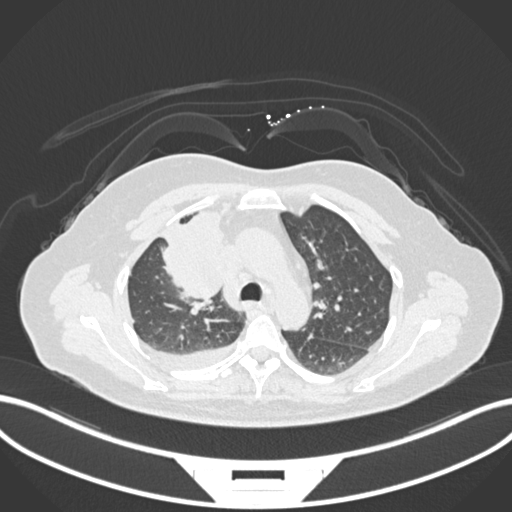
Chest CT, one axial slice. Position 109 of 172 along the scan axis. Reconstruction kernel B30f. 120 kVp. Lung window (W 1500 / L -600 HU). 512 × 512 image matrix. Female patient, age 52 years. Case-level facts recorded for this patient, not image findings: clinical TNM (as recorded): T3 N1 M1.
Structures marked on this image (rectangle marked by the reading radiologist):
- lung tumour (recorded histology: adenocarcinoma): bounding box <157,206,229,309> (left, top, right, bottom; pixels)